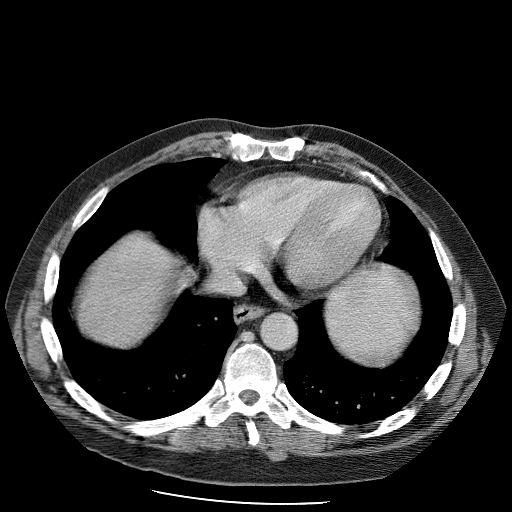
Contrast-enhanced abdominal CT (liver protocol), one axial slice. Soft-tissue window (W 400 / L 40 HU). 512 × 512 image matrix, field of view 400 × 400 mm. From the clinical record (not read from this slice): diagnosis: hepatocellular carcinoma (patient treated with transarterial chemoembolisation; whether this scan precedes or follows treatment is not stated here); TNM stage (as recorded): Stage-II; Child-Pugh class: B; tumour differentiation: moderately differentiated; tumour nodularity: uninodular.
Structures marked on this image (semi-automatic segmentation, software-assisted and operator-edited):
- liver parenchyma outside the tumour (the mass and vessels are separate outlines, so this box may not span the whole liver): bounding box (x1, y1, x2, y2) in pixels: (78, 238, 170, 340)